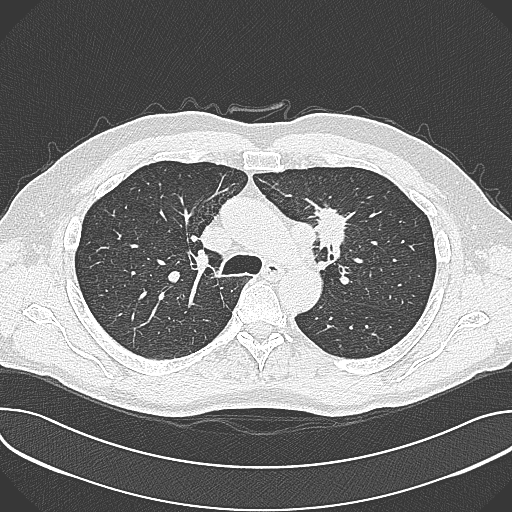
Chest CT (low-dose screening protocol), one axial image, first (baseline) screen, lung window (W 1500 / L -600 HU), 1 mm slice thickness, slice 105 of 361 in the series. Male participant, aged 59 years at enrolment.
Expert-annotated lung lesion, bounding box <302,196,362,257> (left, top, right, bottom; pixels). The screening reader recorded 2 non-calcified nodules or masses ≥4 mm on this exam (left upper lobe, left upper lobe); which of them this box marks is not recorded.